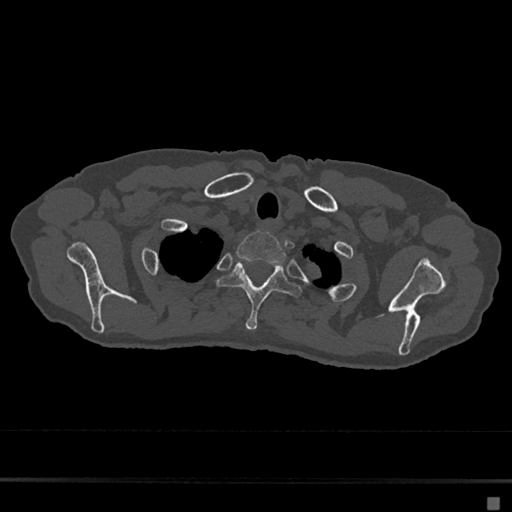
CT including the spine, one axial slice. Slice 584 of 797 in the series (ordered by position). 120 kVp. Bone window (W 1800 / L 400 HU). 0.5 mm slice thickness. 512 × 512 image matrix. Female patient, age 68 years. From the clinical record (not read from this slice): primary cancer: renal.
Outlined on this slice (semi-automatic segmentation, software-assisted and operator-edited):
- T1 vertebra: box from (x=236, y=231) to (x=286, y=263) px
- T2 vertebra: (x=216, y=257)–(x=301, y=331)